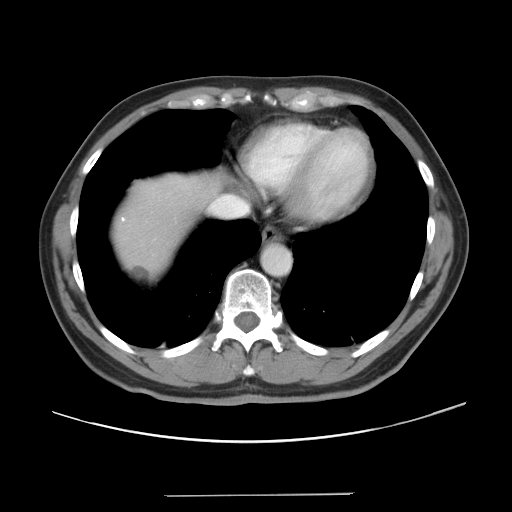
Contrast-enhanced abdominal CT, one axial slice. Position 37 of 43 along the scan axis. Reconstruction kernel STANDARD. 120 kVp. Soft-tissue window (W 400 / L 40 HU). 512 × 512 image matrix. Male patient, age 65 years. From the clinical record (not read from this slice): diagnosis: colorectal cancer liver metastases, imaged before liver resection; multiple liver metastases: no; largest metastasis: 3.8 cm; chemotherapy before resection: yes.
Annotated regions visible in this slice (manually delineated by an expert):
- liver: bounding box <114,175,222,280> (left, top, right, bottom; pixels)
- planned liver remnant (the part of the liver to remain after resection): <114,175,223,264>
- liver metastasis: <133,266,150,280>